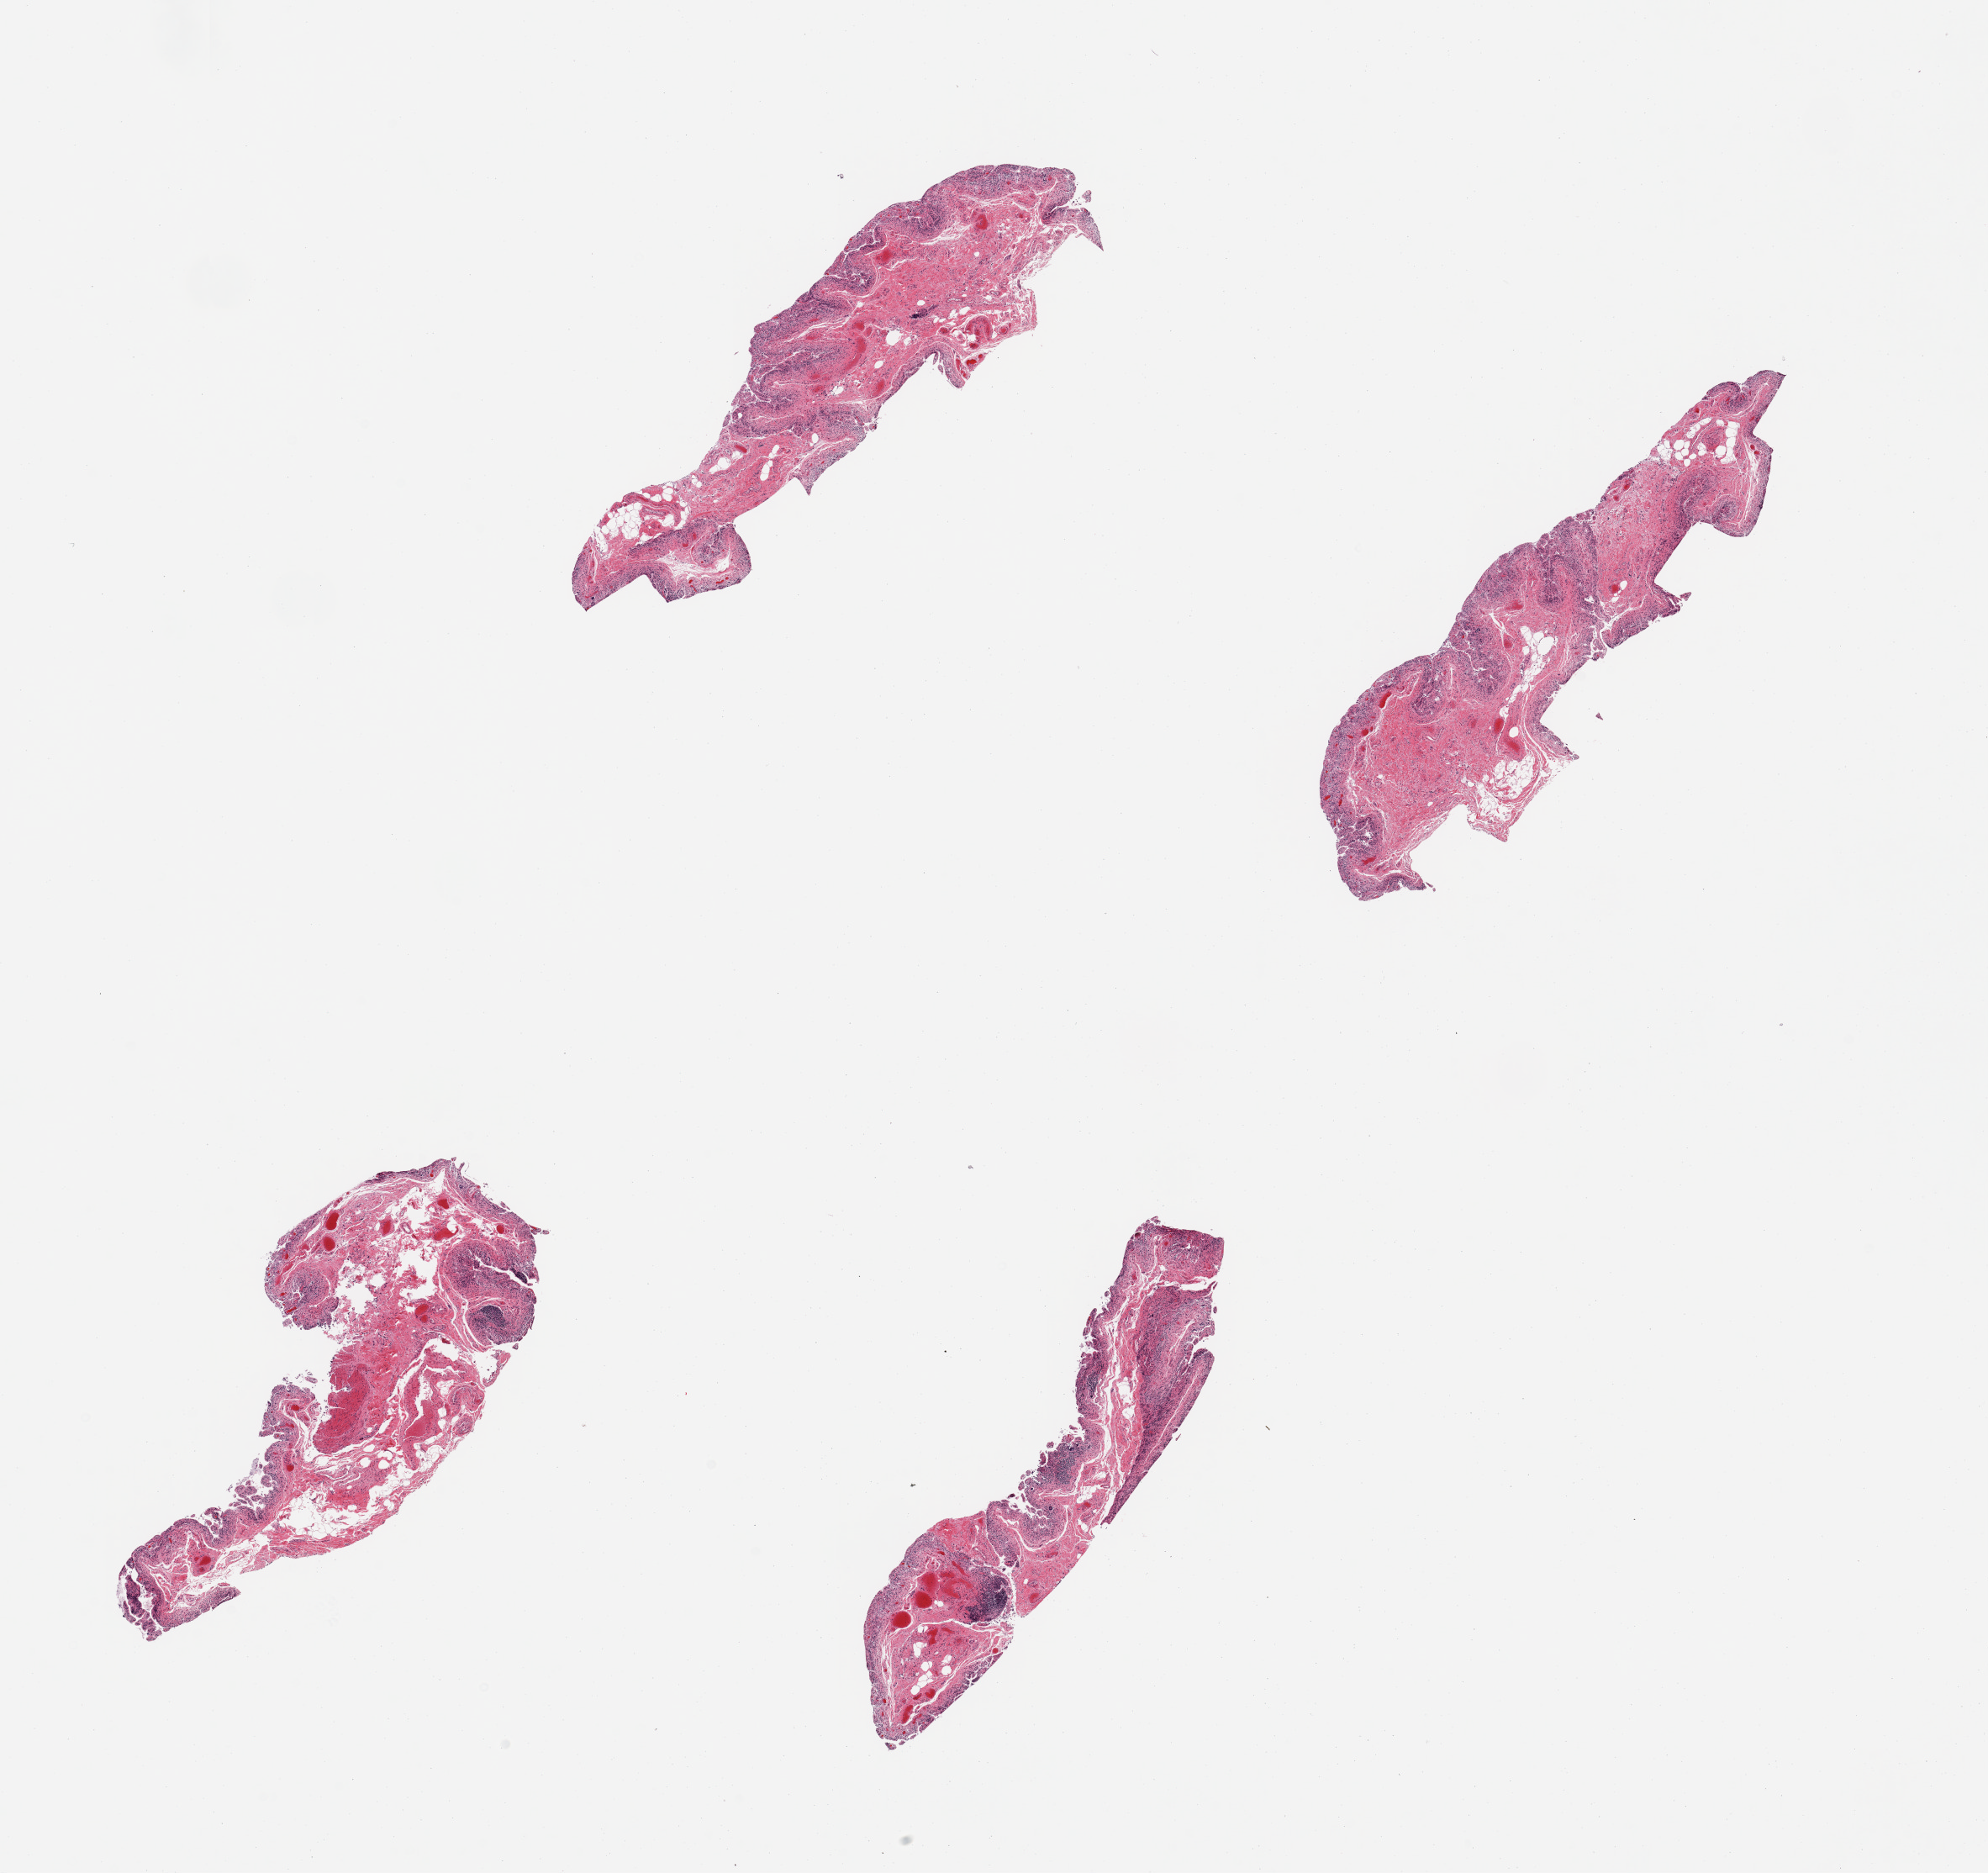
Whole-slide image, hematoxylin and eosin (H&E) stain, brightfield, low-resolution overview of the scanned area, about 18.7 x 17.6 mm (from a 20x scan). PAXgene-fixed, paraffin-embedded tissue. Target tissue: ileum. Tissue donor sample. Donor: female.
Review note (as recorded): 4 pieces; autolyzed tissue with 2 very small (0.4mm) lymphoid nodules.